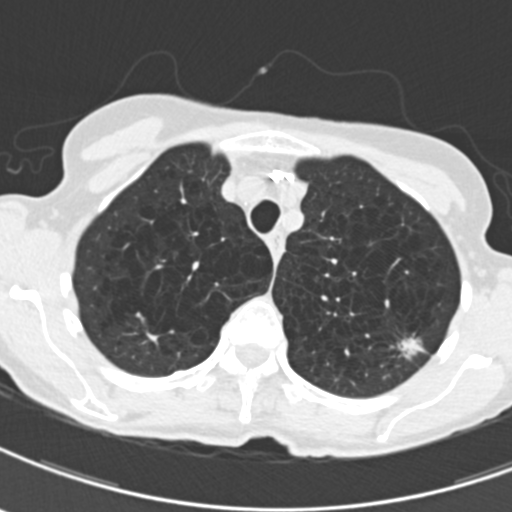
Low-dose screening chest CT, one axial slice. Slice 160 of 203 in the series (ordered by position). Reconstruction kernel B30f. Lung window (W 1500 / L -600 HU). 512 × 512 image matrix.
Structures marked on this image (outlined manually by an expert reader):
- lesion 1 (tumor, upper lobe of left lung): bounding box [x1, y1, x2, y2] px = [396, 337, 424, 360]